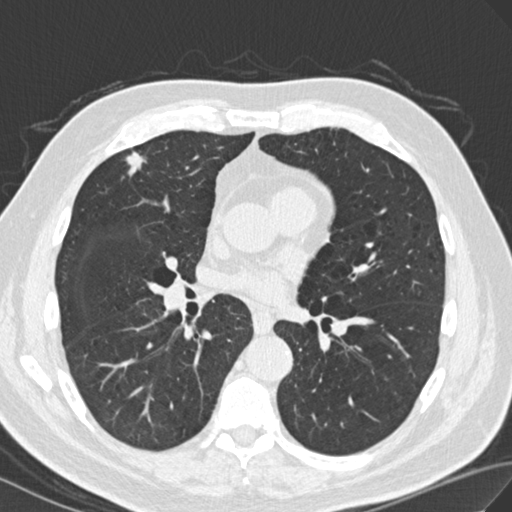
Low-dose screening chest CT, axial slice; second screening round (one year after baseline); lung window (W 1500 / L -600 HU); standard (soft-tissue) reconstruction kernel (B30f). Male, age 69 years at enrolment. Current smoker at enrolment.
Expert reader's lesion annotation, box from (x=109, y=140) to (x=161, y=188) px. The screening reader recorded 3 non-calcified nodules or masses ≥4 mm on this exam (right upper lobe, right lower lobe, right lower lobe); which of them this box marks is not recorded. Official screen result: positive, other. Participant outcome: lung cancer diagnosed 183 days after this screen — adenocarcinoma, NOS, right upper lobe, moderately differentiated (G2), stage IIA (AJCC 6th edition), 20 mm at pathology.